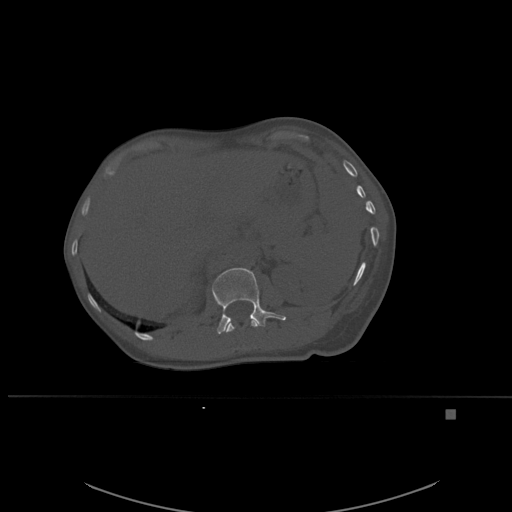
CT including the spine, one axial slice. Position 266 of 537 along the scan axis. Bone window (W 1800 / L 400 HU). 1.5 mm slice thickness. 512 × 512 image matrix, field of view 440 × 440 mm. Female patient, age 45 years. From the clinical record (not read from this slice): primary cancer: lung.
Outlined on this slice (semi-automatically segmented with operator editing):
- L1 vertebra: bounding box (x1, y1, x2, y2) in pixels: (212, 268, 286, 334)
- T12 vertebra: (225, 319, 260, 333)